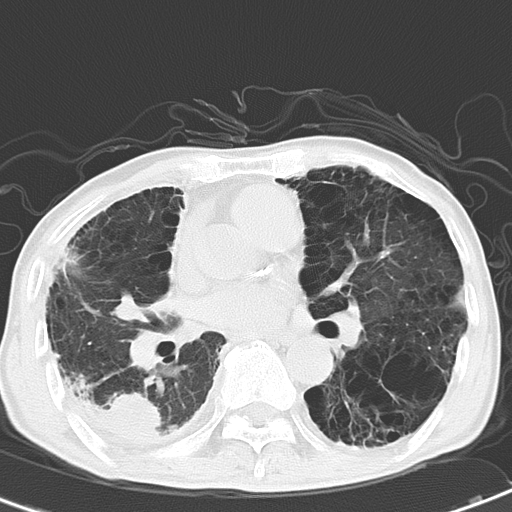
Chest CT, one axial slice; position 24 of 51 along the scan axis; reconstruction kernel B70f; 120 kVp; lung window (W 1500 / L -600 HU); 6 mm slice thickness; 512 × 512 image matrix, field of view 279 × 279 mm. Patient: male, 67 years. From the clinical record (not read from this slice): clinical TNM (as recorded): T2 N3 M1.
Annotated regions visible in this slice (rectangle marked by the reading radiologist):
- lung tumour (recorded histology: adenocarcinoma): bounding box (x1, y1, x2, y2) in pixels: (105, 383, 168, 447)